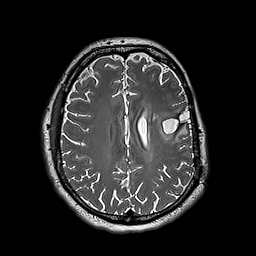
Brain MRI from a brain-tumour surgery series, one axial slice; slice 78 of 192 in the series (ordered by position); 1 mm slice thickness; 256 × 256 image matrix. From the clinical record (not read from this slice): histopathology: Astrocytoma; WHO grade: 3; IDH mutation: yes; tumour location: Left Insular.
Structures marked on this image (outlined manually by an expert reader):
- tumour: bounding box (x1, y1, x2, y2) in pixels: (153, 109, 171, 141)